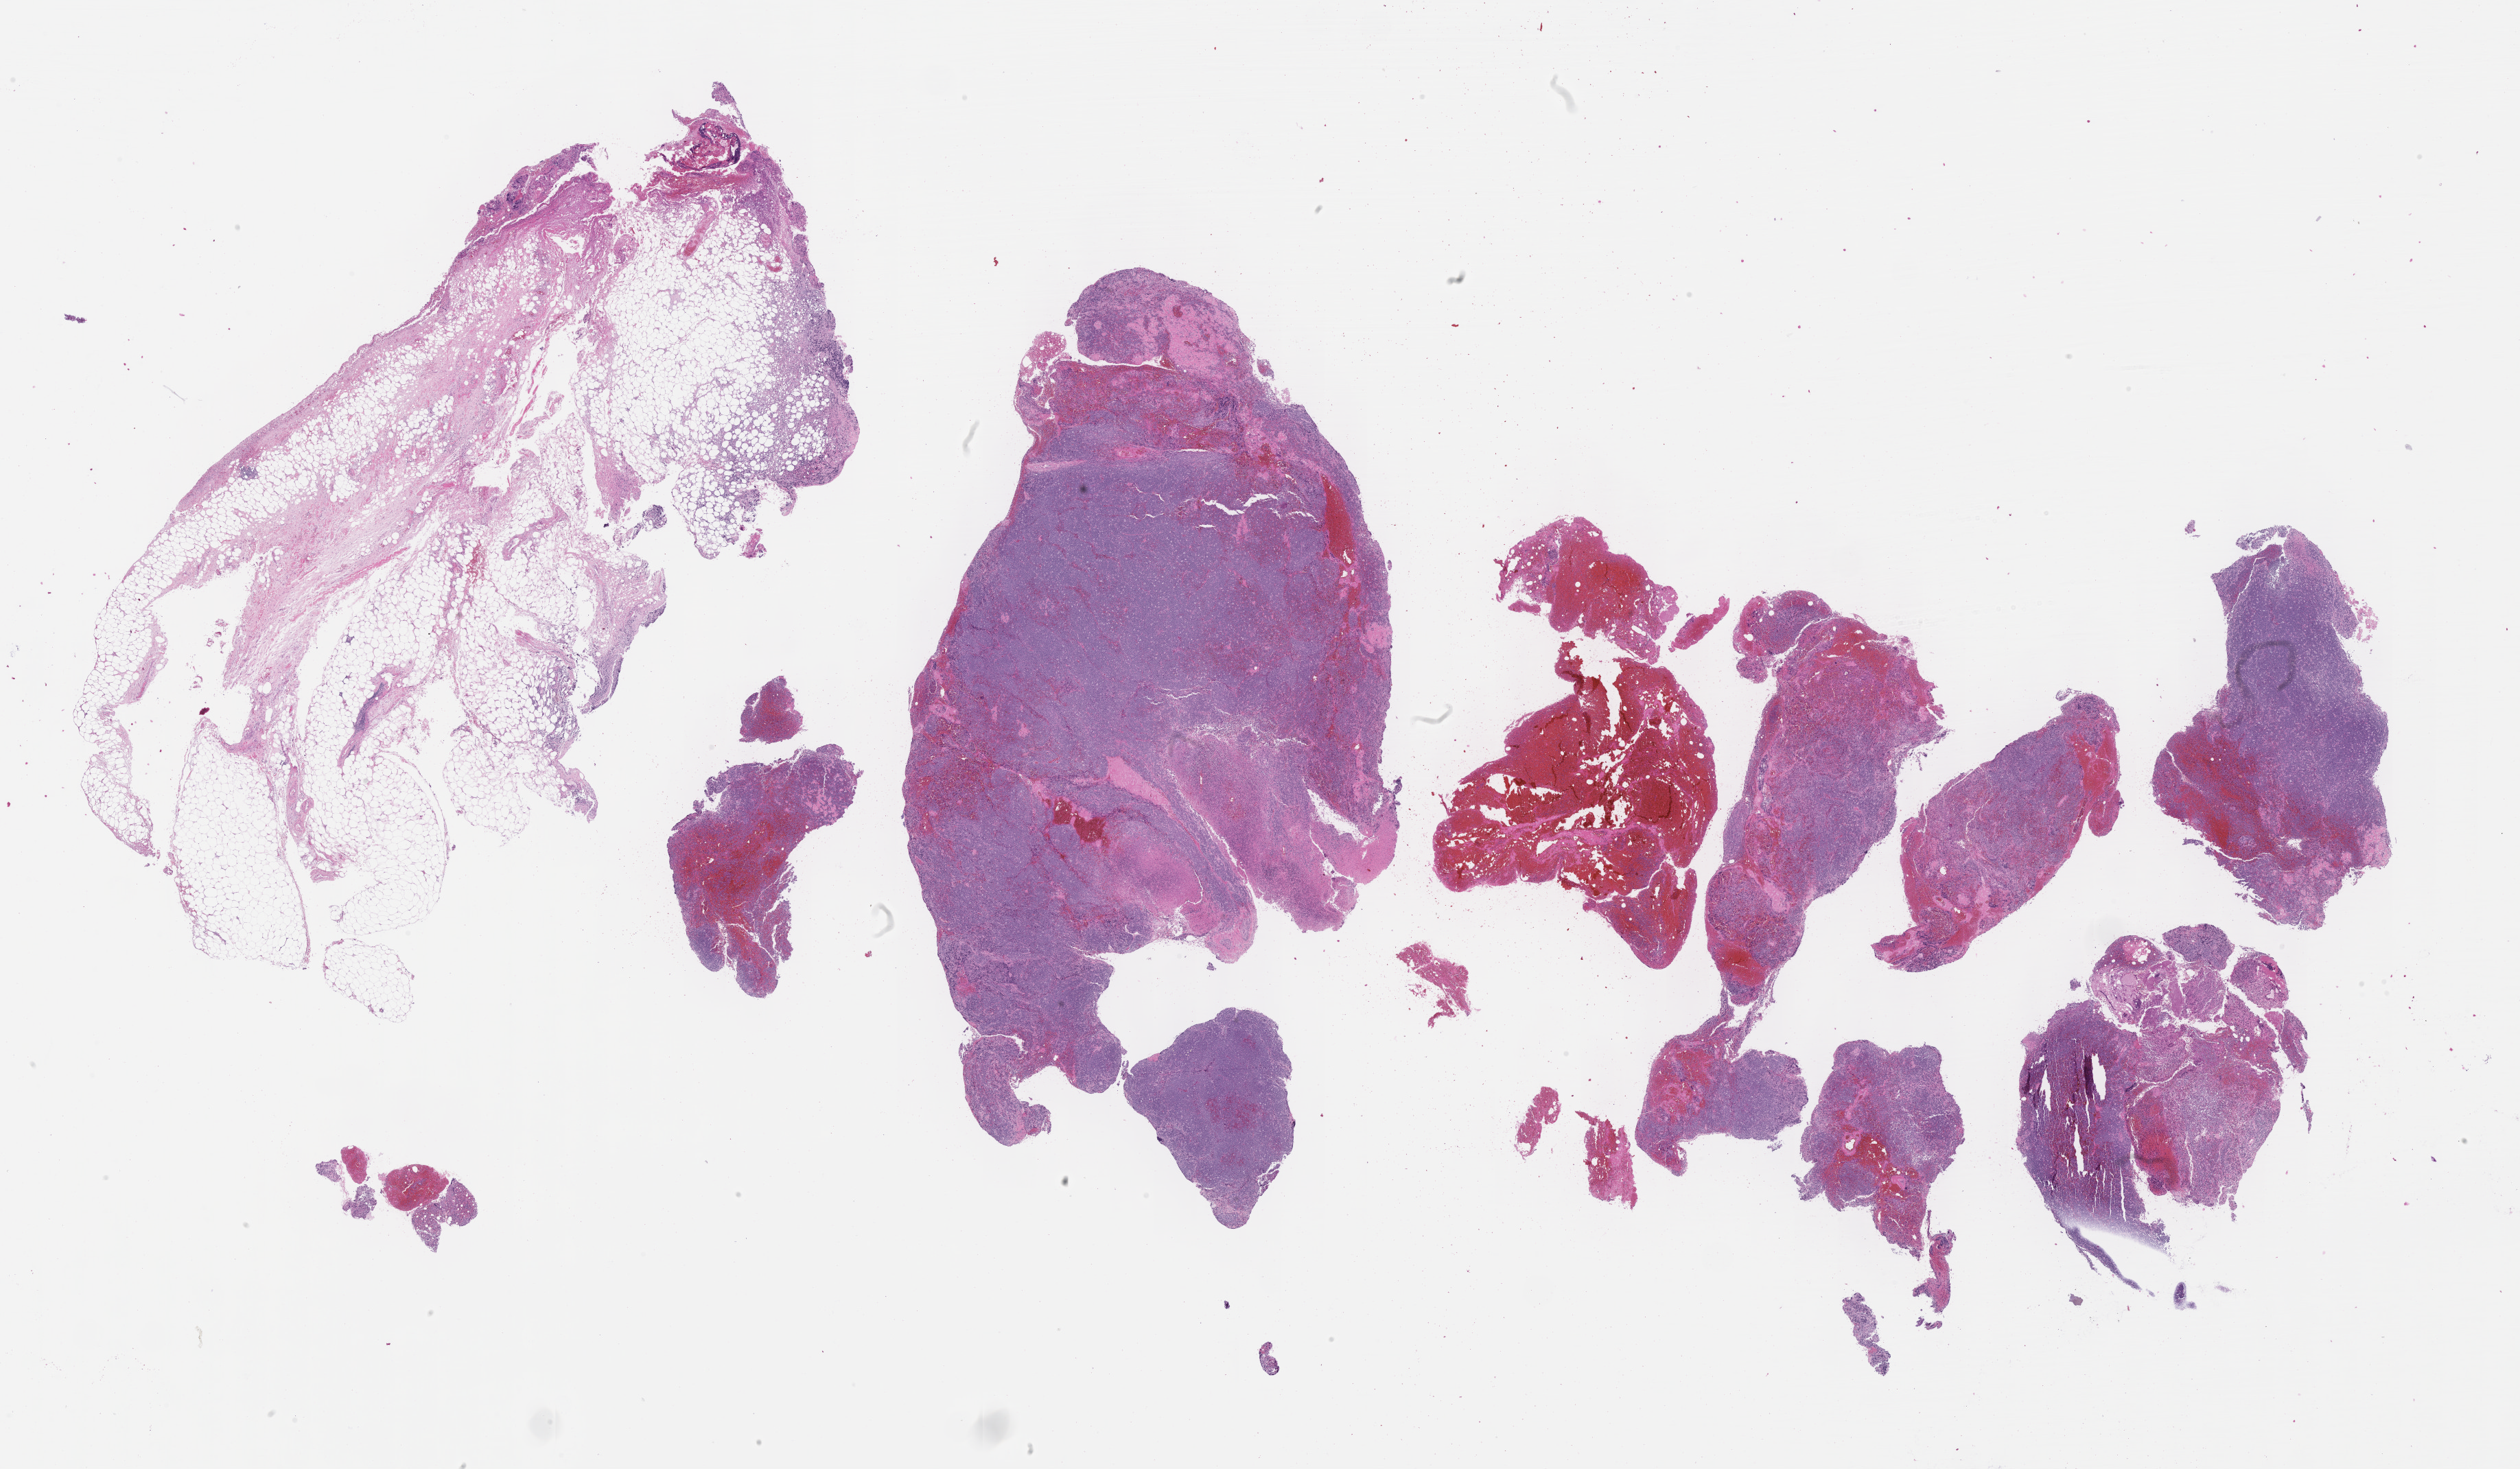
H&E whole-slide image — a low-resolution overview of the entire scanned area, about 29.7 x 17.3 mm; formalin-fixed, paraffin-embedded (FFPE) tissue; primary tumor; anatomic site: abdominal lymph node. Male patient, 27 years old. Composition of this section per pathologist review: tumor cells 60%, tumor nuclei 90%, stromal cells 30%, necrosis 5%, normal cells 5%. Infiltration values recorded for this section: lymphocyte infiltration 20%, monocyte infiltration 30%, neutrophil infiltration 10%.
Ann Arbor stage (patient): Stage IV. Section: top of the tissue portion. Histologic diagnosis: Burkitt lymphoma, NOS.